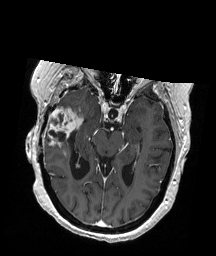
Brain MRI from a brain-tumour surgery series, one axial slice; position 117 of 192 along the scan axis; T1-weighted post-contrast; 216 × 256 image matrix, field of view 211 × 250 mm. From the clinical record (not read from this slice): histopathology: Glioblastoma; WHO grade: 4; IDH mutation: no; tumour location: Right Temporal.
Outlined on this slice (manually delineated by an expert):
- tumour: bounding box [x1, y1, x2, y2] px = [43, 106, 83, 146]